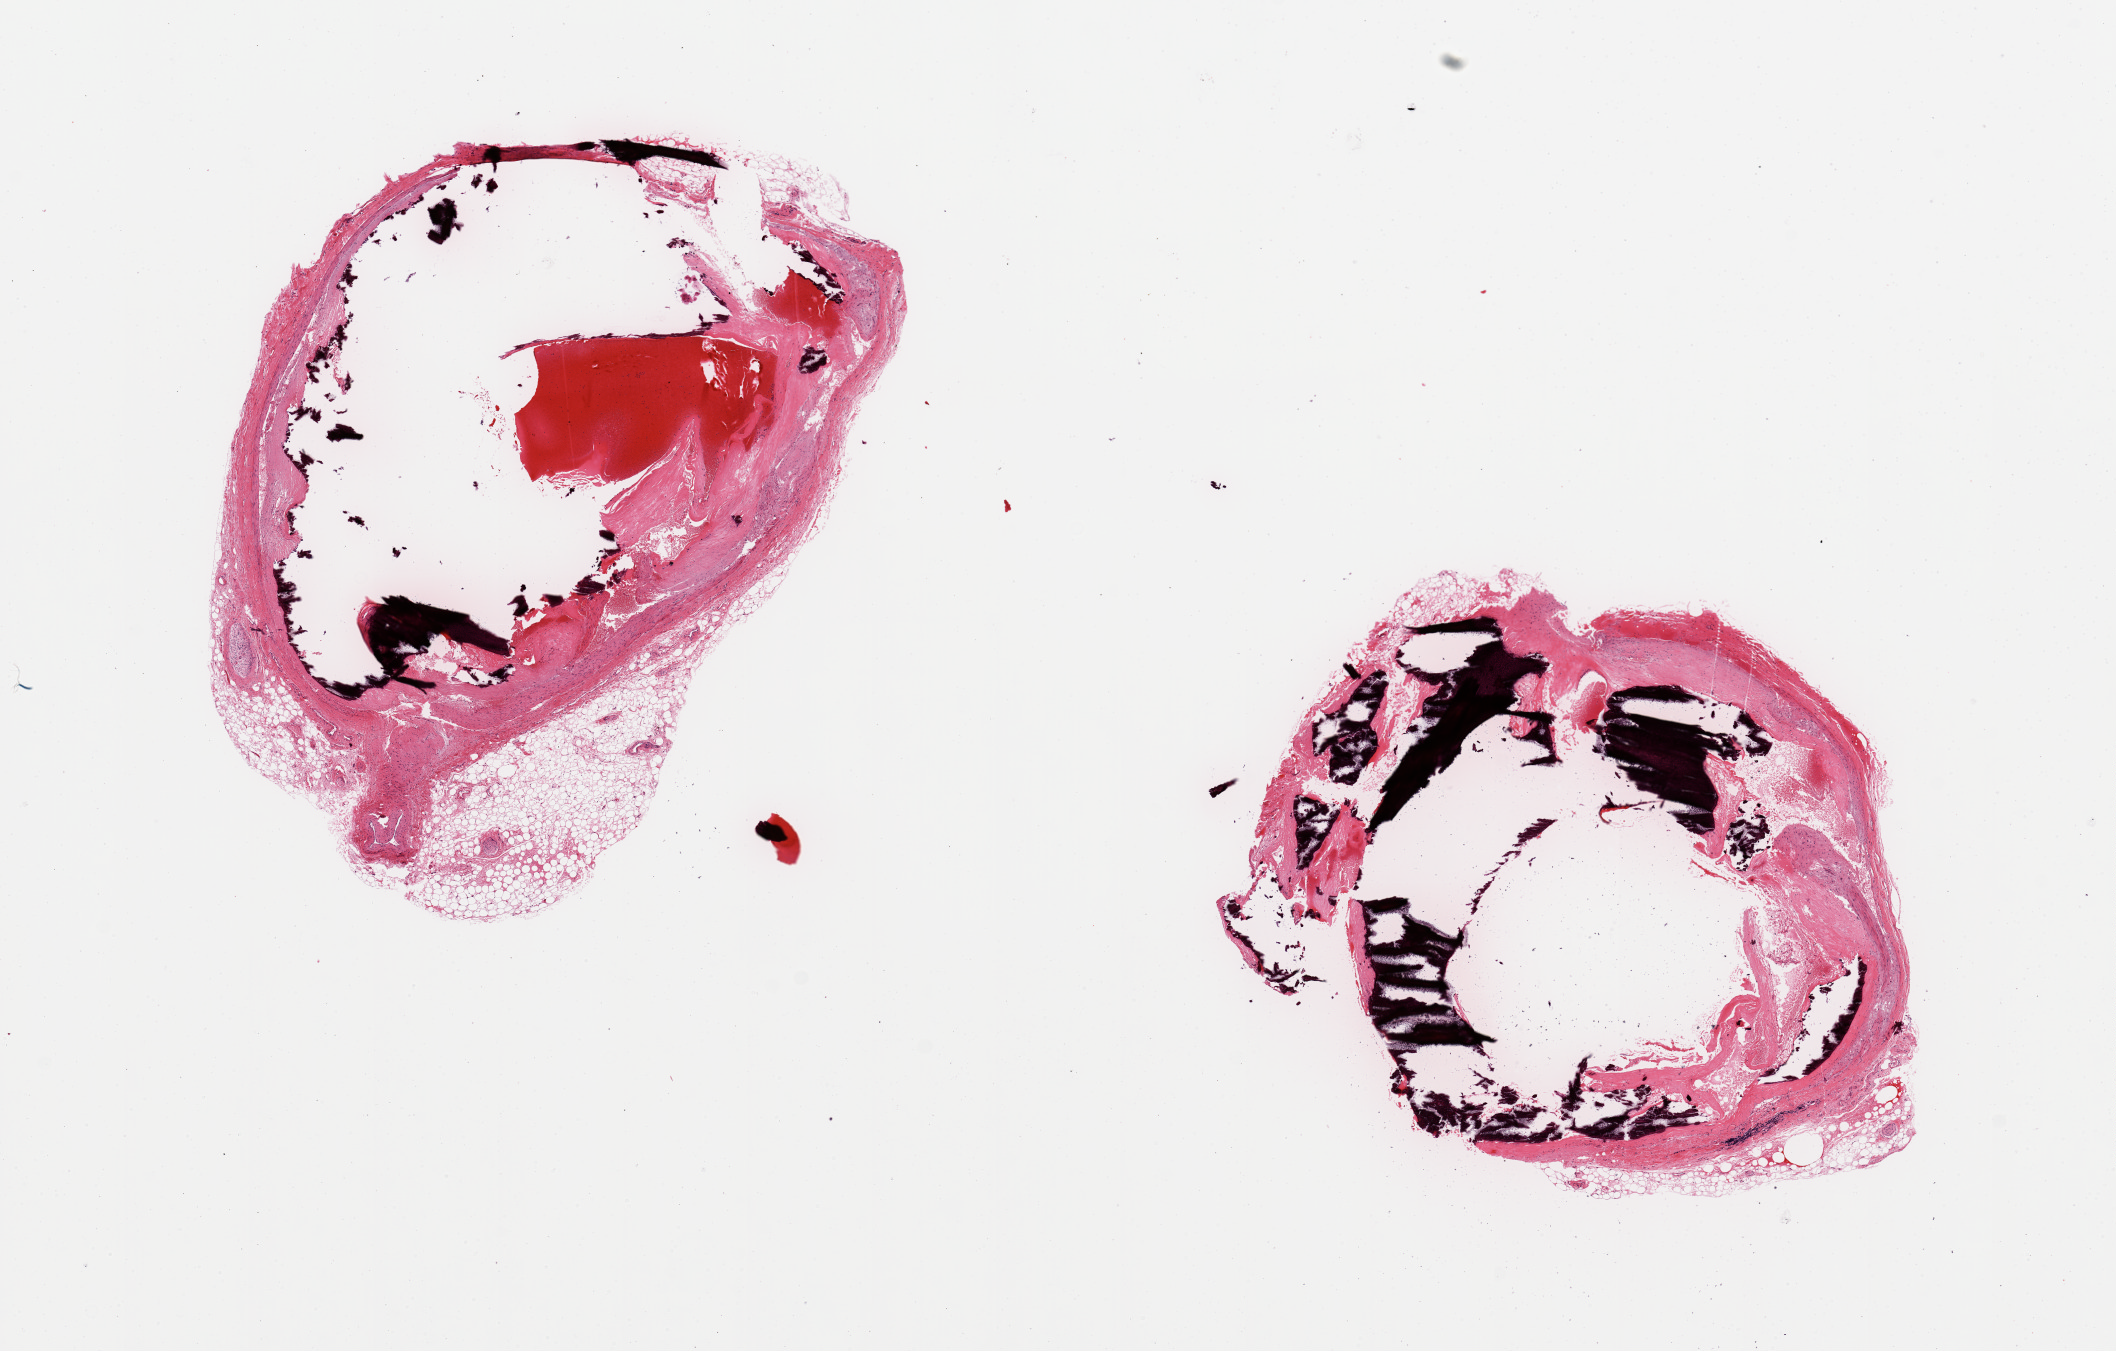
Whole-slide image, H&E stain — whole scanned area (about 16.7 x 10.7 mm) shown as a low-resolution overview. Female donor.
Specimen: PAXgene-fixed paraffin-embedded (PFPE) section; section of coronary artery (target tissue); tissue donor sample.